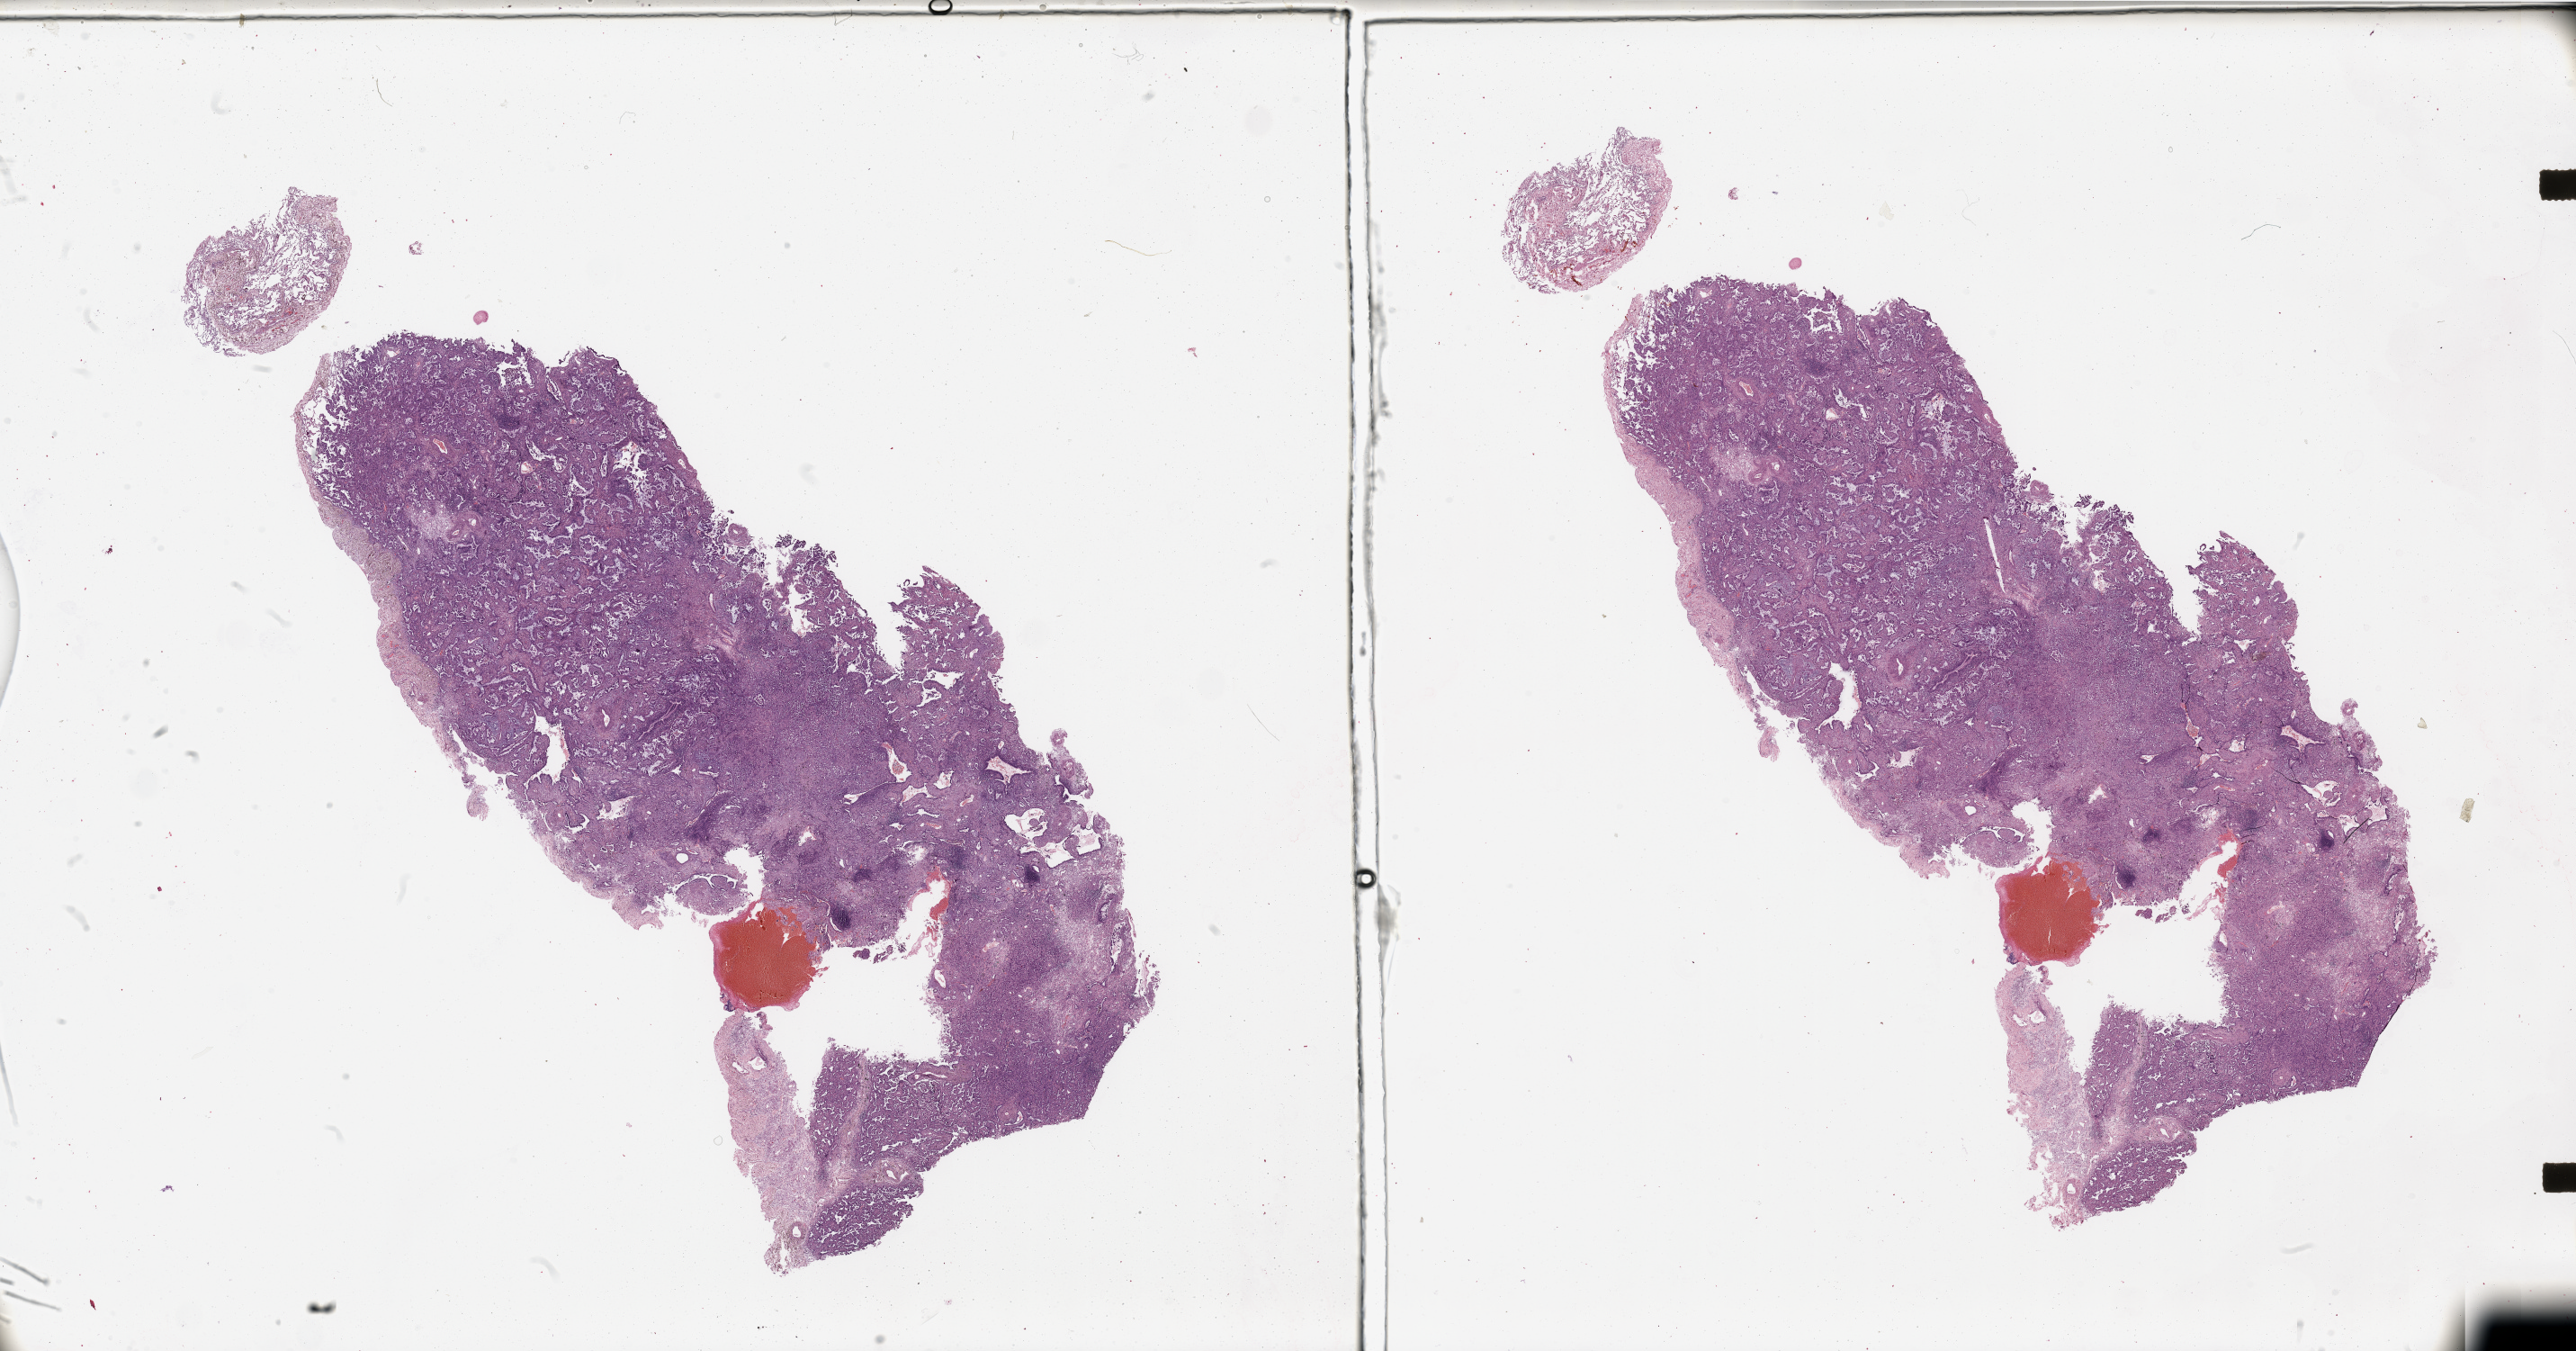
Whole-slide histology image, Hematoxylin and eosin (H&E) stained, a low-resolution overview of the entire scanned area, about 45.3 x 23.7 mm (slide scanned at 20x). Tumour tissue sample, sampled site: lung. 70-year-old female patient. Histologic grade: G2 (moderately differentiated). Slide review estimates, as recorded: tumour nuclei 70%, necrosis 0%.
AJCC pathologic stage: IB. Primary tumour site (as recorded): left lower lobe. Diagnosis: Adenocarcinoma, NOS.